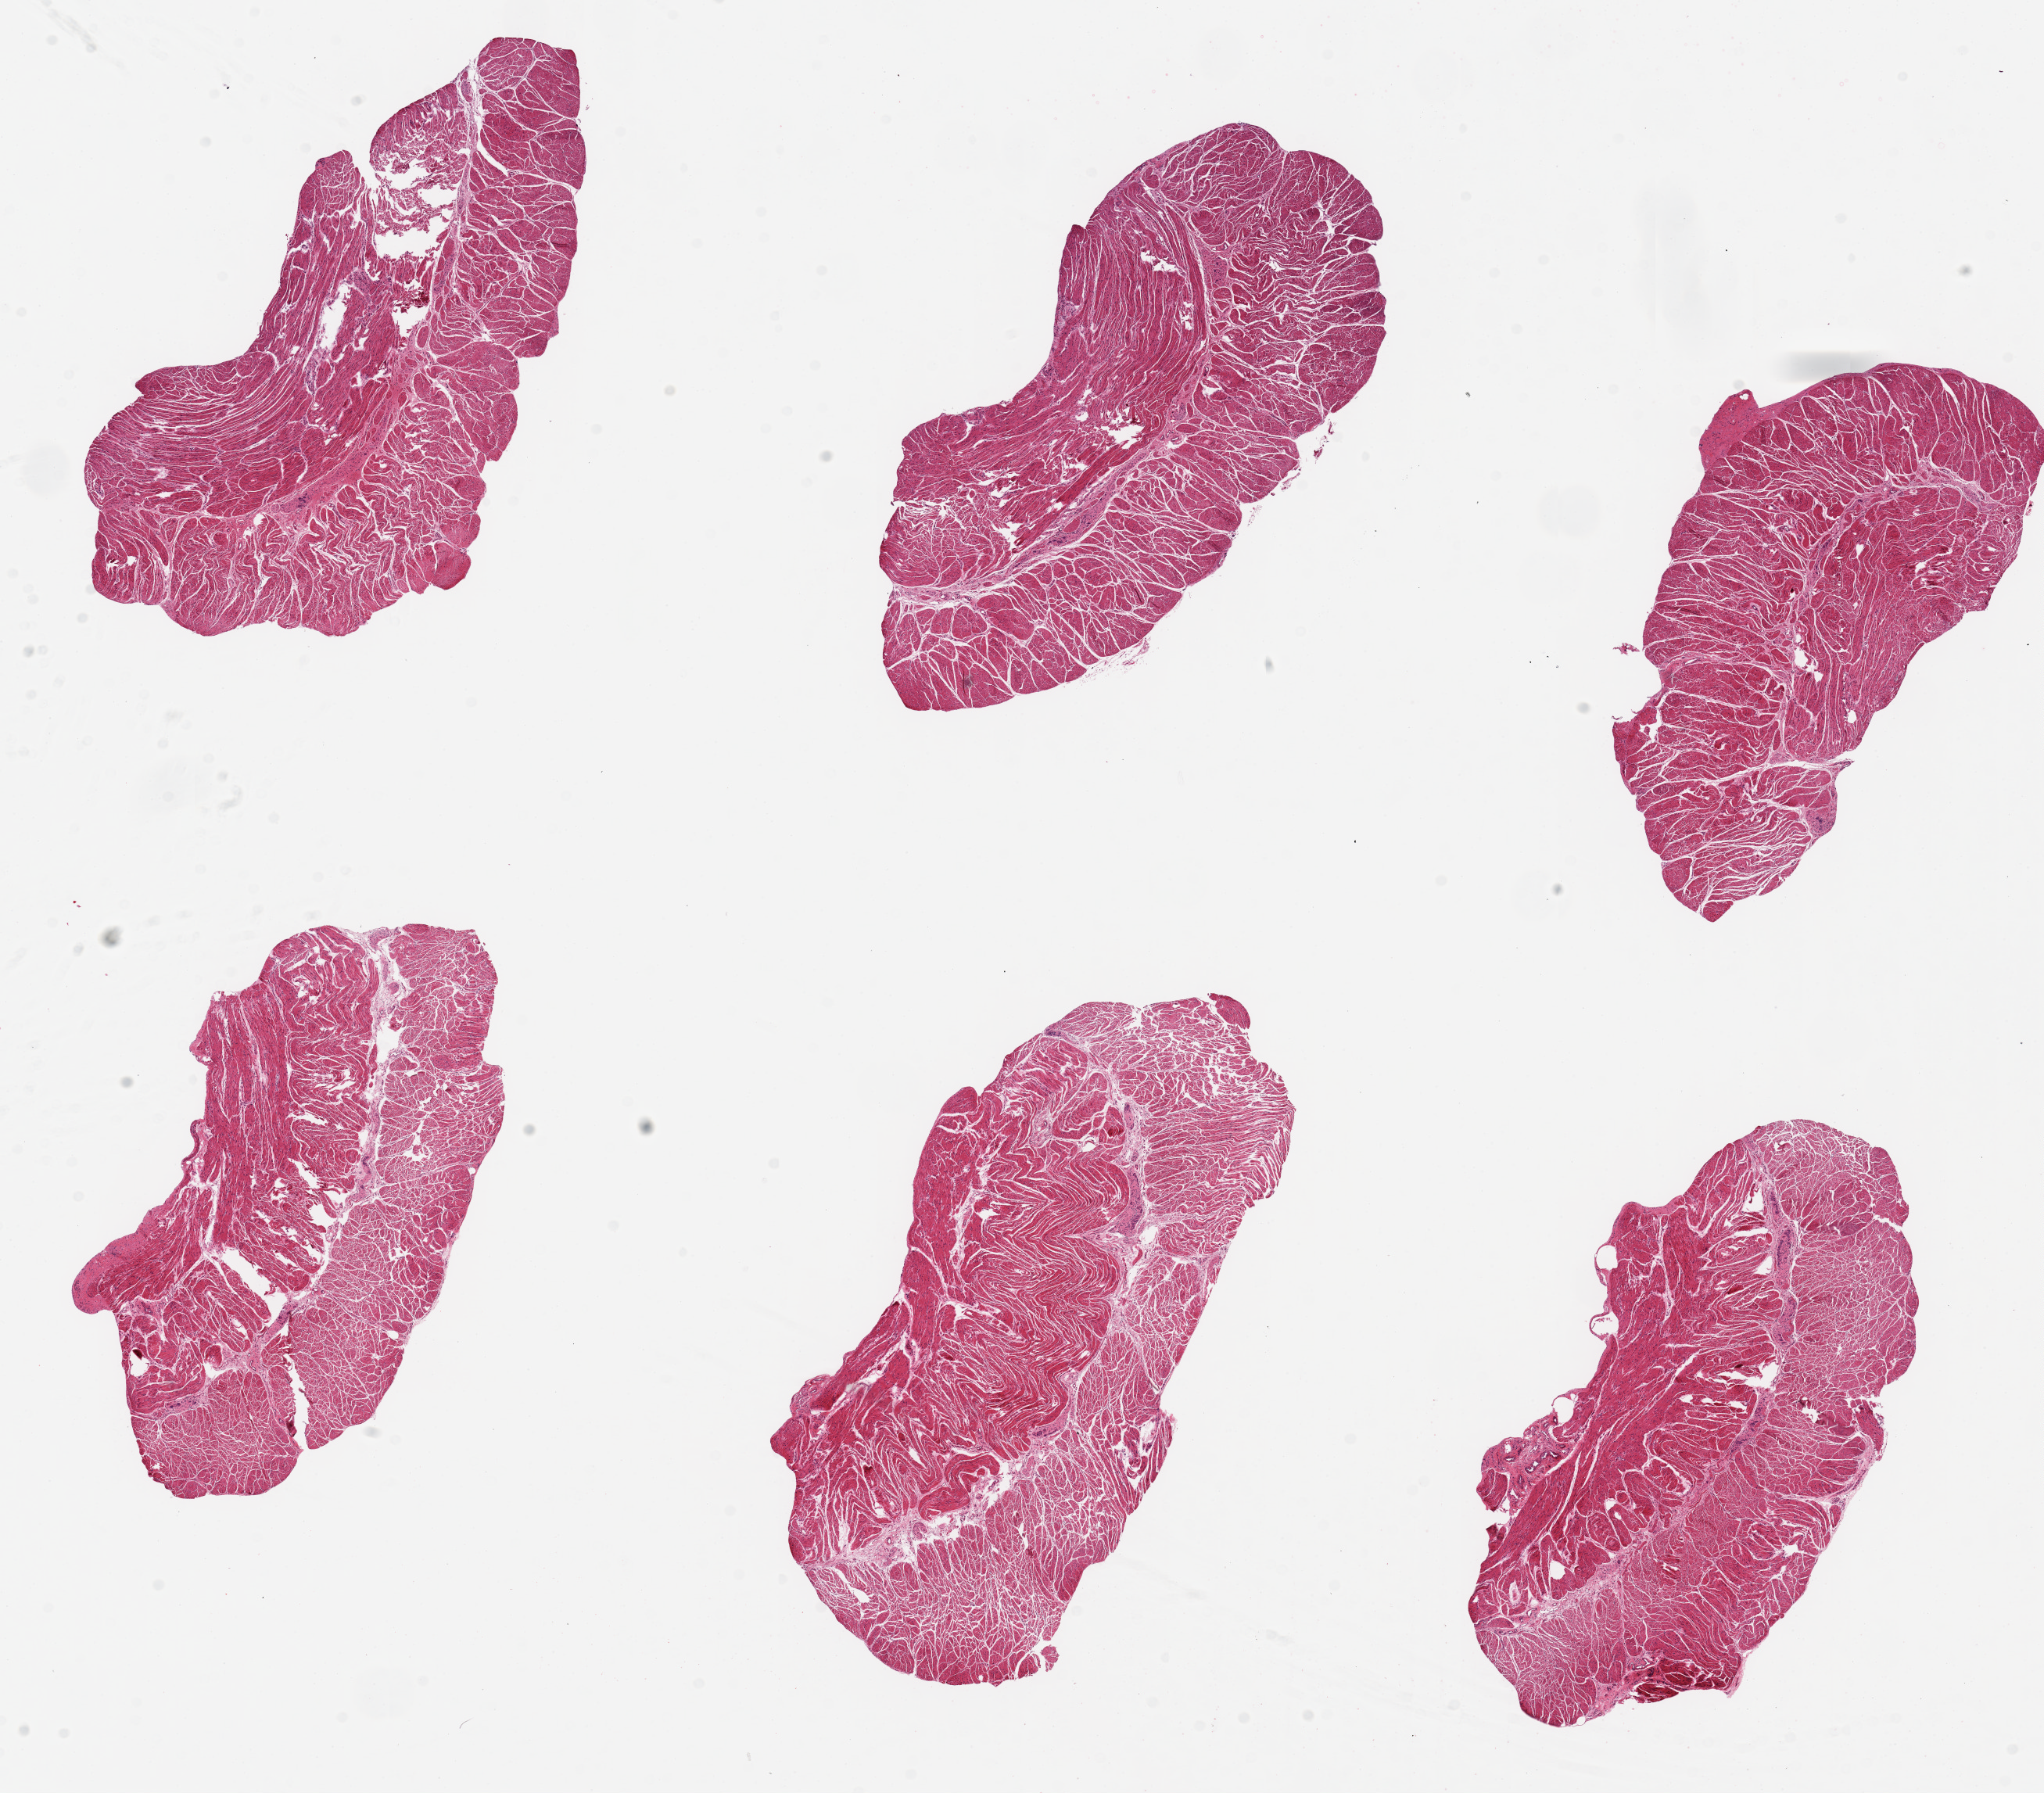
Digitized hematoxylin and eosin (H&E)-stained section — whole scanned area (about 20.7 x 18.1 mm) shown as a low-resolution overview. PAXgene-fixed, paraffin-embedded tissue. Target tissue: esophageal muscle. Tissue donor sample. Donor: female.
- pathologist's review note for this sample: 6 pieces, up to 7.5x4mm; all muscularis, good specimens